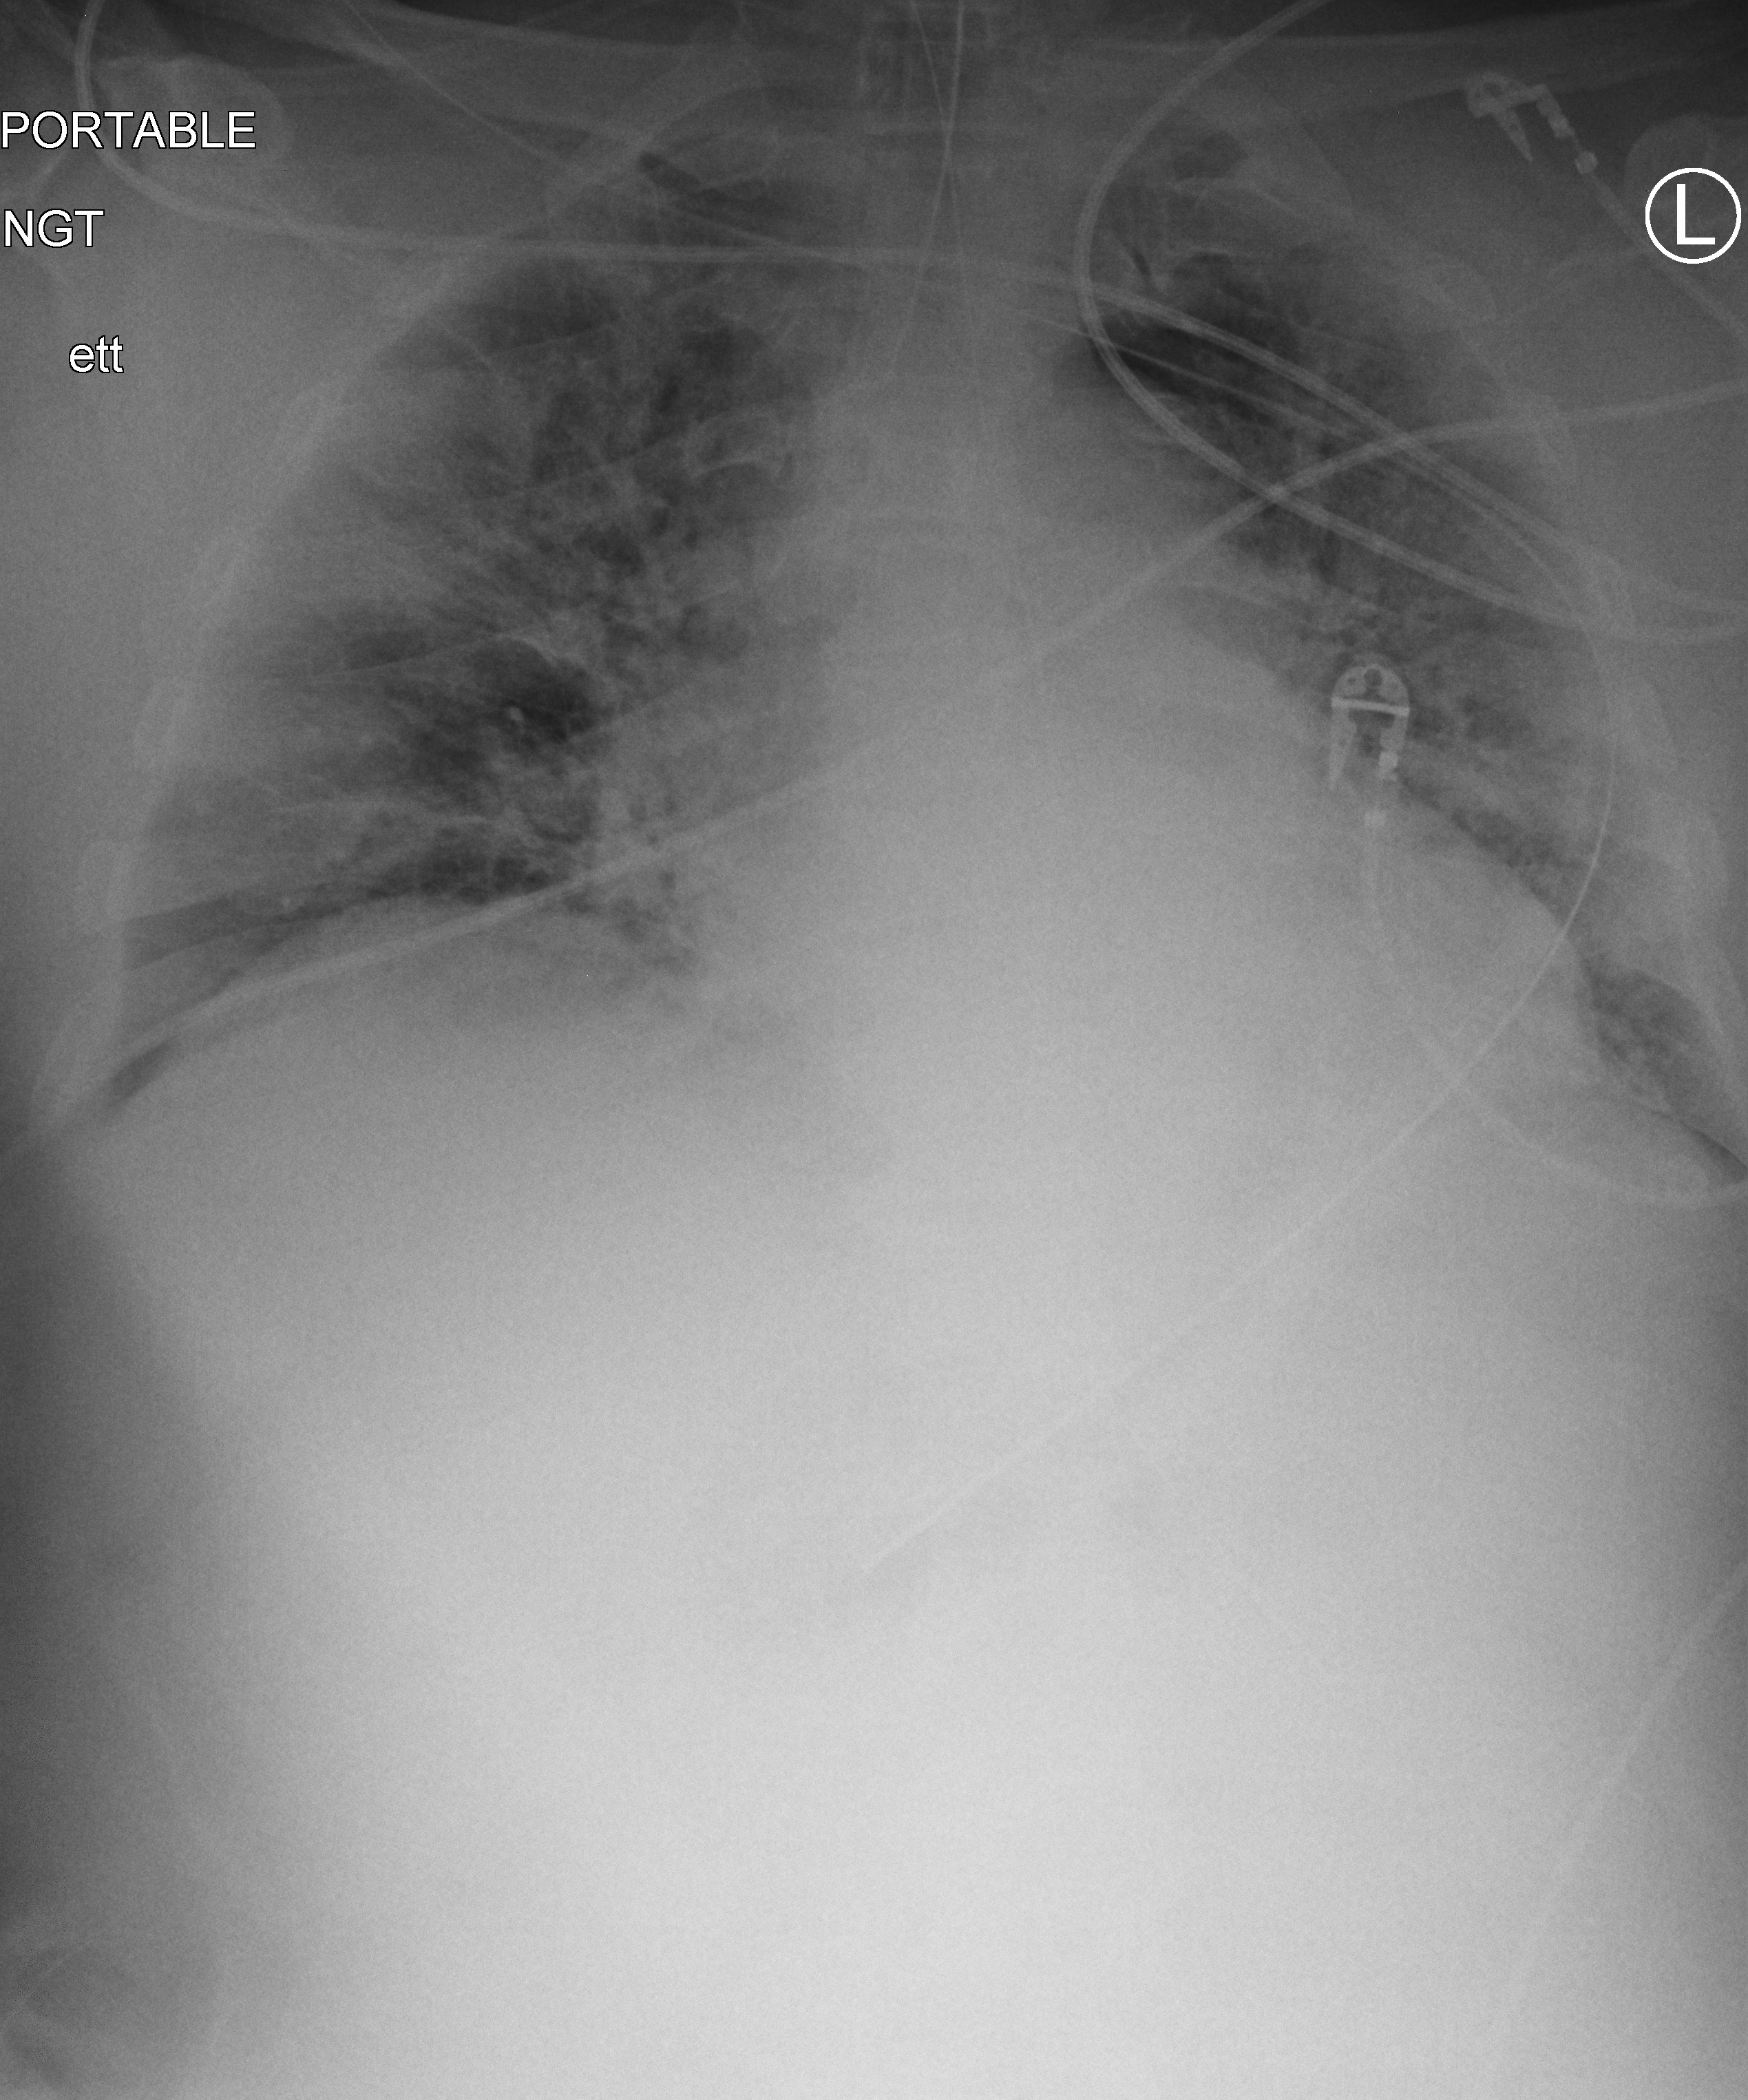
Portable chest radiograph; anteroposterior (AP) projection. Patient hospitalised with COVID-19; male, aged 60–74 years.
Admission-level facts for this patient (not findings on this image; timing relative to this image not recorded):
- admitted to intensive care during this hospital stay: yes
- COPD (admission record): no
- other chronic lung disease (admission record): no